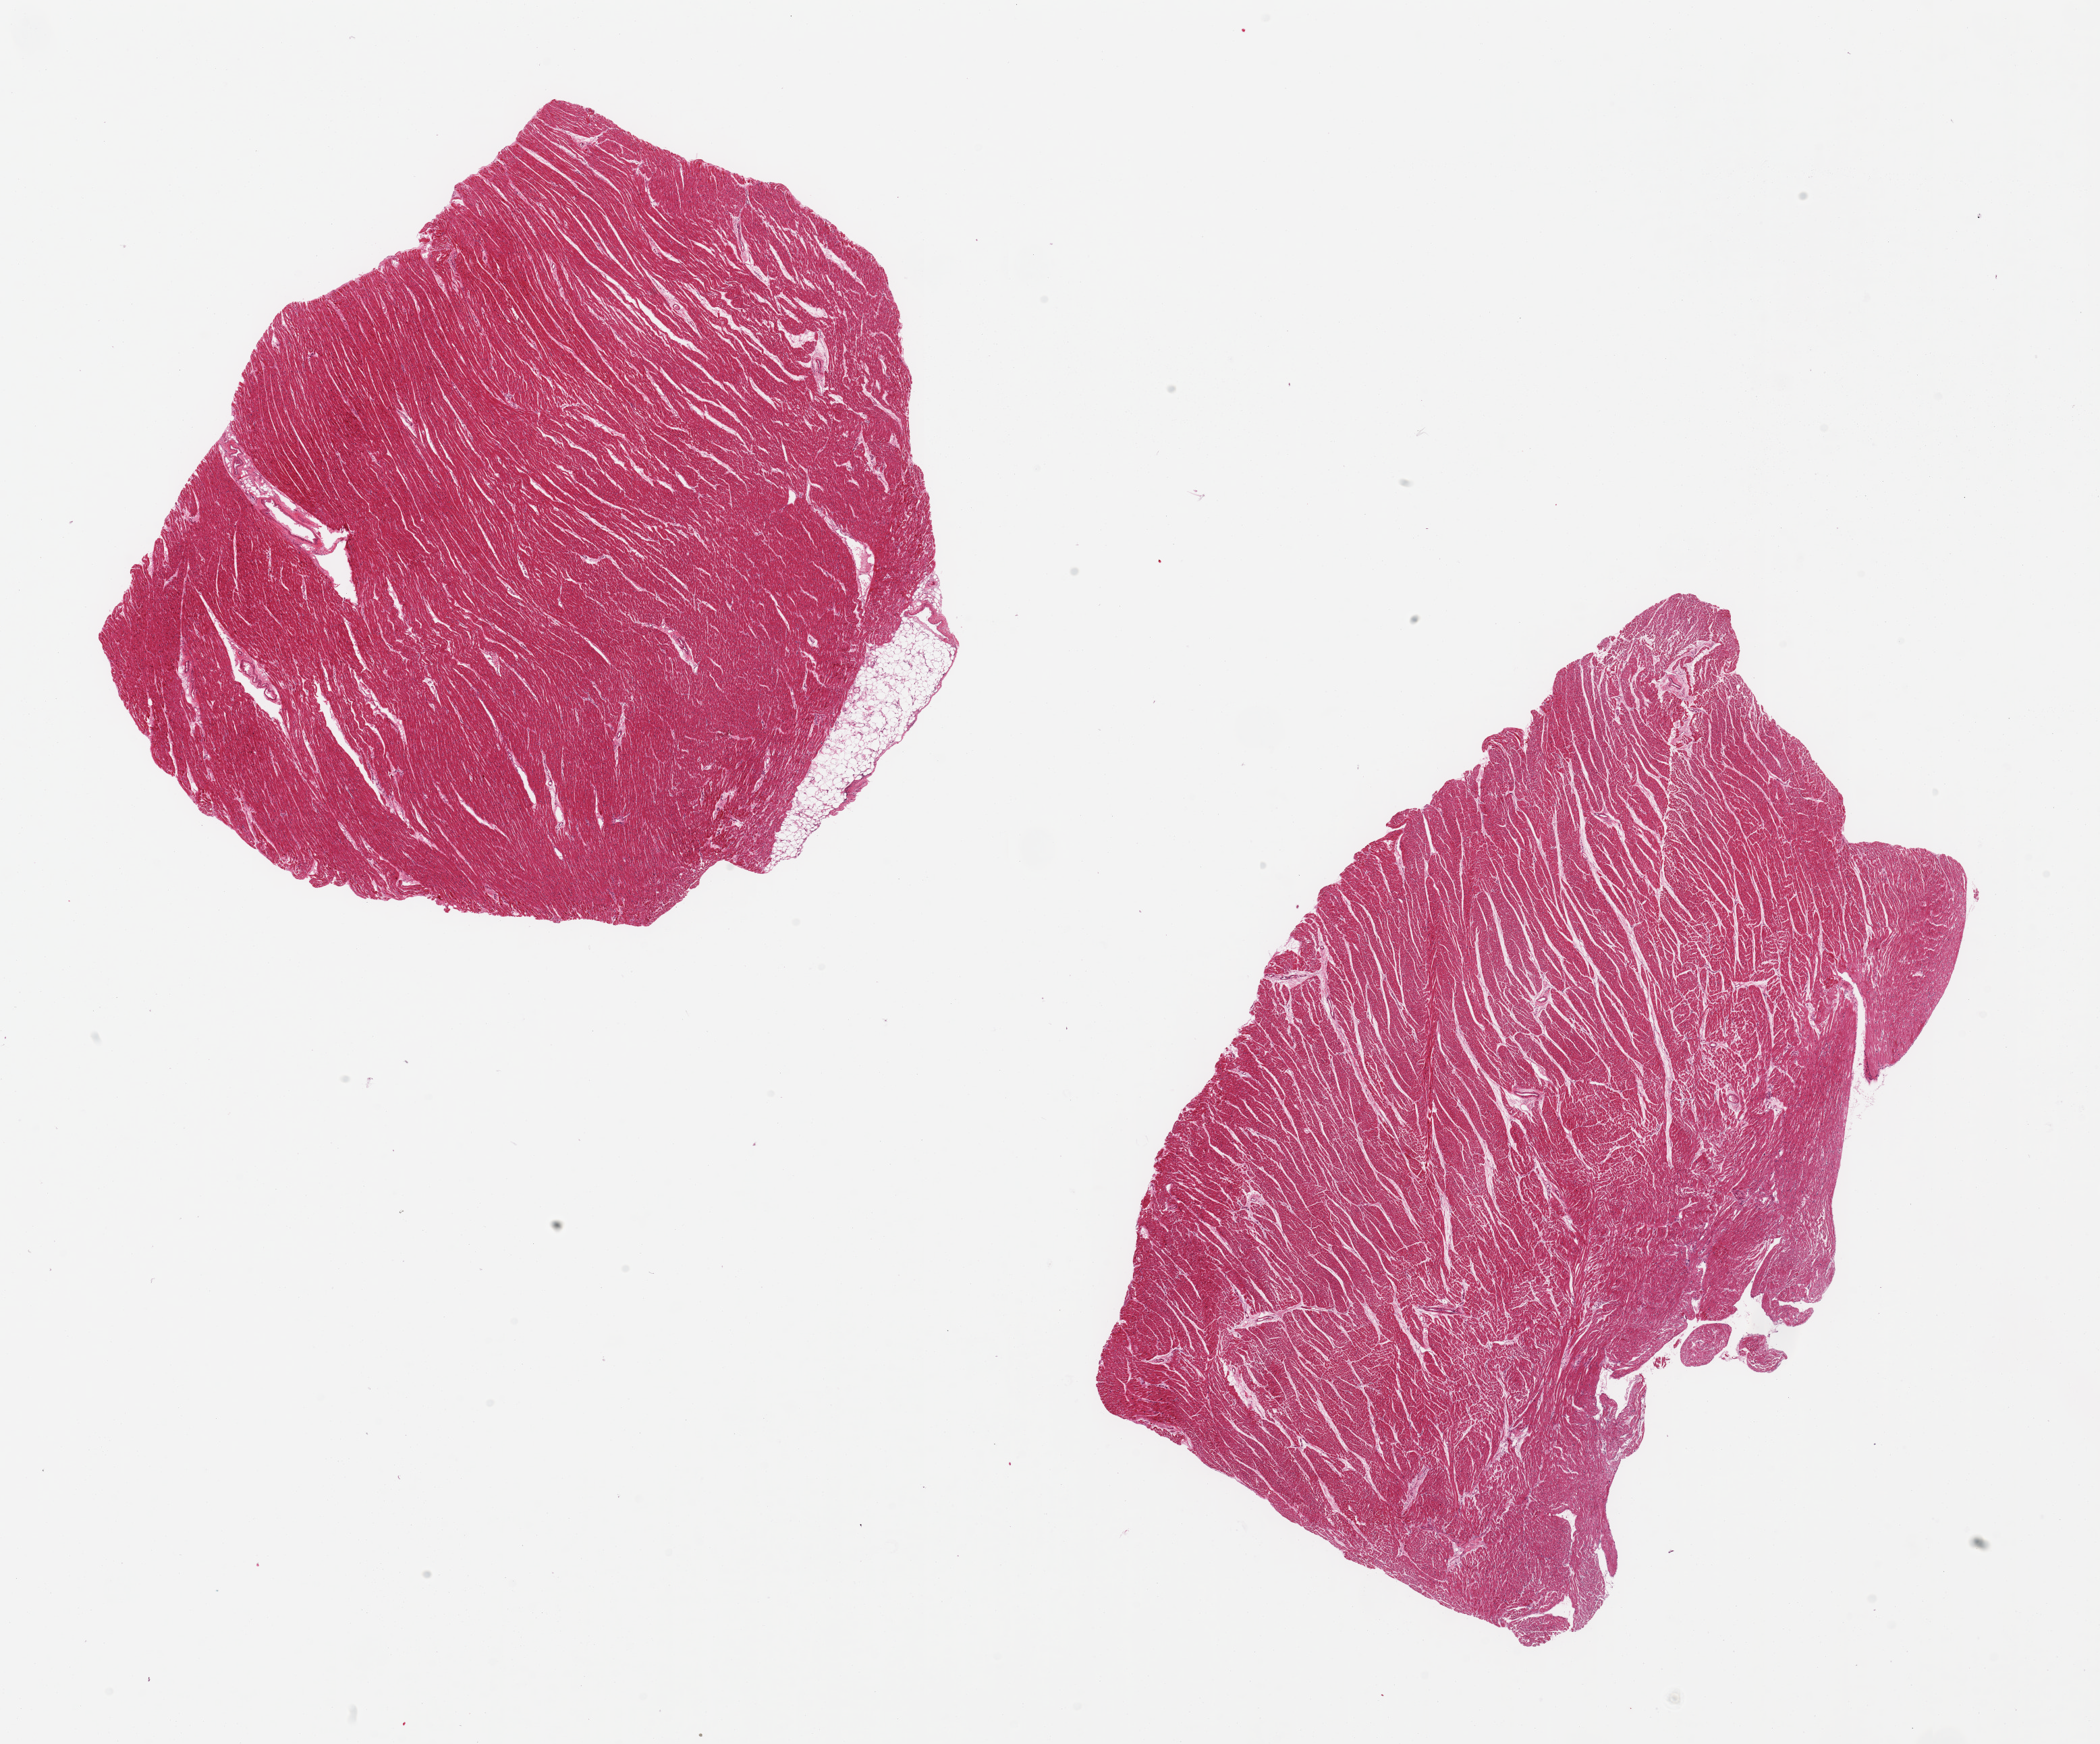
Hematoxylin and eosin (H&E) whole-slide image, brightfield, low-resolution overview of the scanned area, about 24.6 x 20.4 mm; PAXgene-fixed paraffin-embedded (PFPE) section; section of heart (target tissue); donor tissue sample. Donor sex: female.
• reviewer comment on this tissue sample: 2 pieces, minimal interstitial fibrosis/ischemic damage